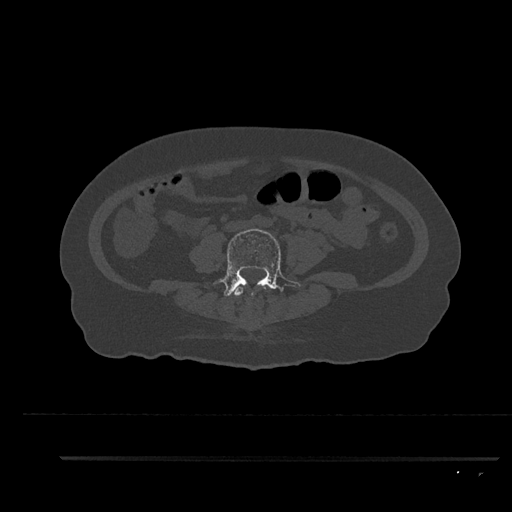
CT including the spine, one axial slice; position 33 of 797 along the scan axis; bone window (W 1800 / L 400 HU); 512 × 512 image matrix. Patient: female, 44 years. Case-level facts recorded for this patient, not image findings: primary cancer: renal.
Outlined on this slice (semi-automatic segmentation, software-assisted and operator-edited):
- L3 vertebra: box from (x=234, y=285) to (x=266, y=296) px
- L4 vertebra: (x=212, y=229)–(x=300, y=301)